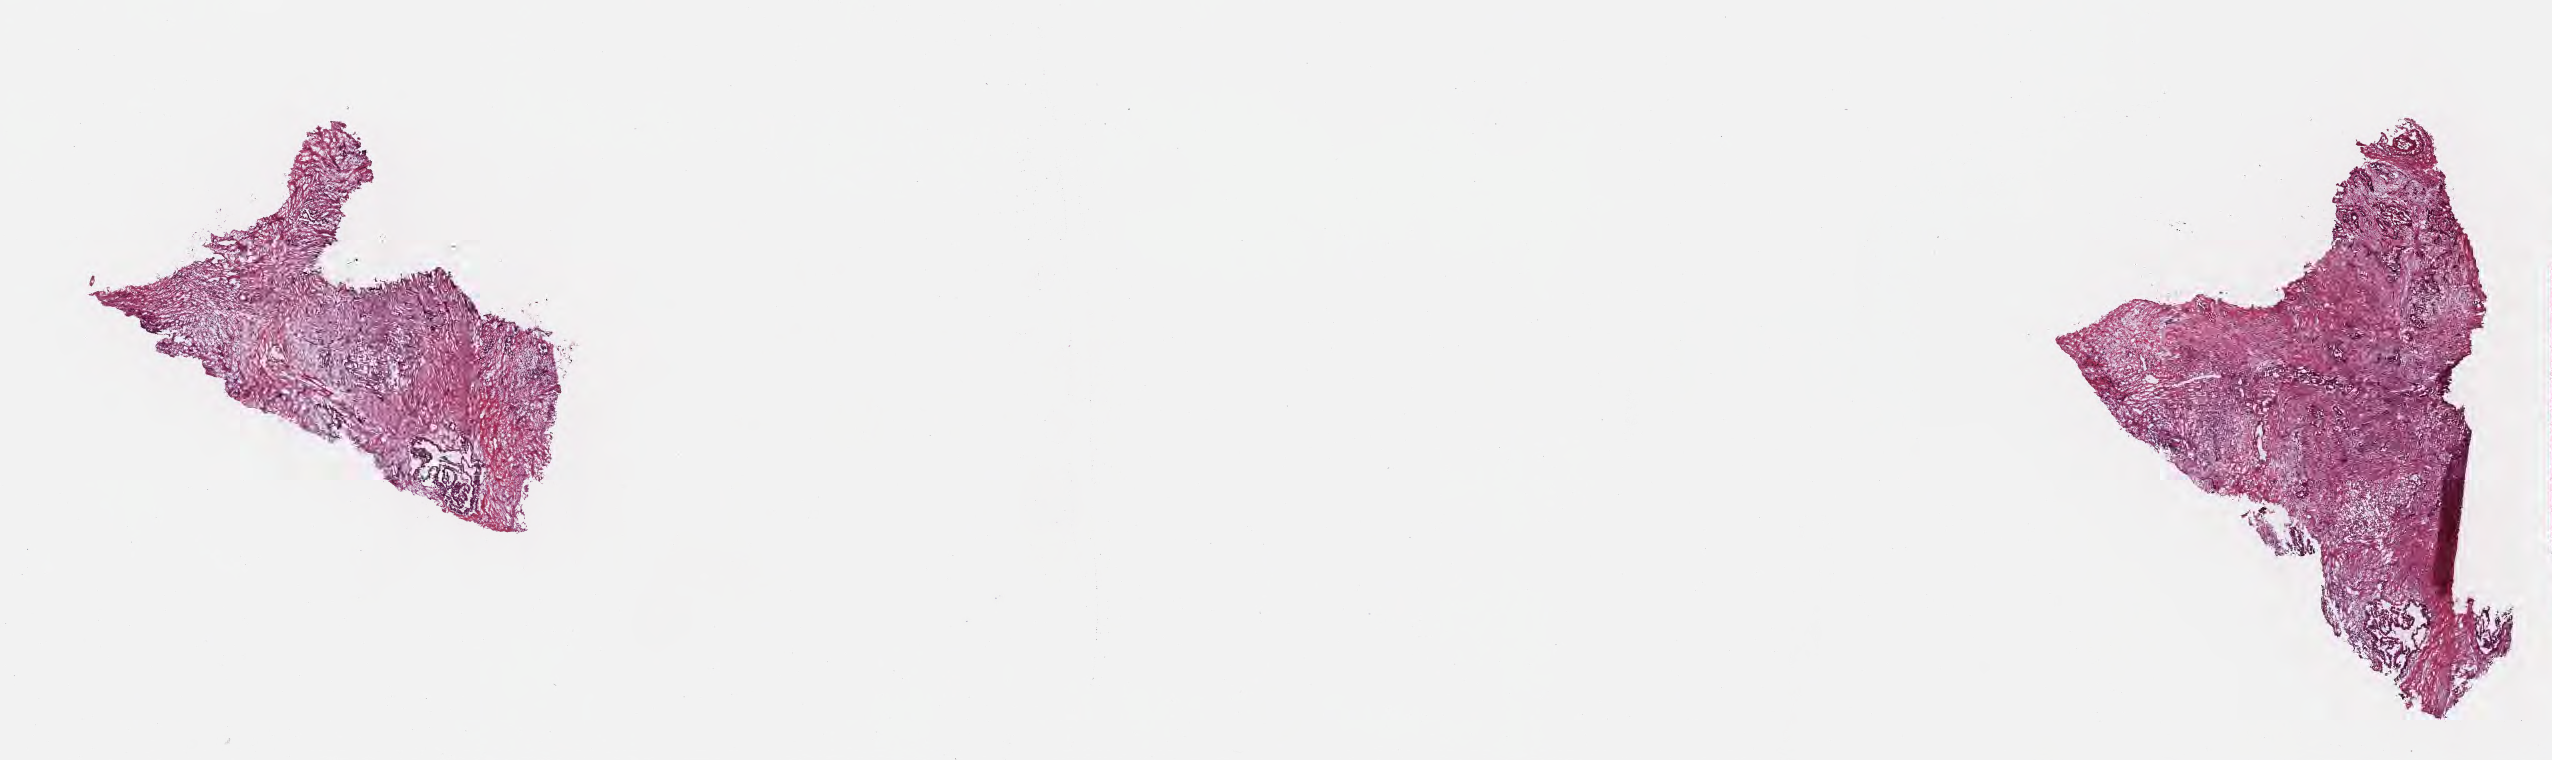
Whole-slide image, haematoxylin and eosin stain, shown as a low-resolution overview of the whole scanned area (about 20.6 x 6.1 mm), frozen section (tissue freezing medium), specimen: primary tumor, anatomic site: head of pancreas. Male, age 74 years at initial diagnosis. Tumor grade: G3 (poorly differentiated). Pathologist review of this section (percent, as recorded): tumor cells 13%, tumor nuclei 18%, stromal cells 86%, necrosis 1%, normal cells 0%. Inflammatory infiltration, as recorded: lymphocyte infiltration 75%, monocyte infiltration 2%, neutrophil infiltration 0%.
Diagnosis: Infiltrating duct carcinoma, NOS. AJCC pathologic stage: Stage IIB.